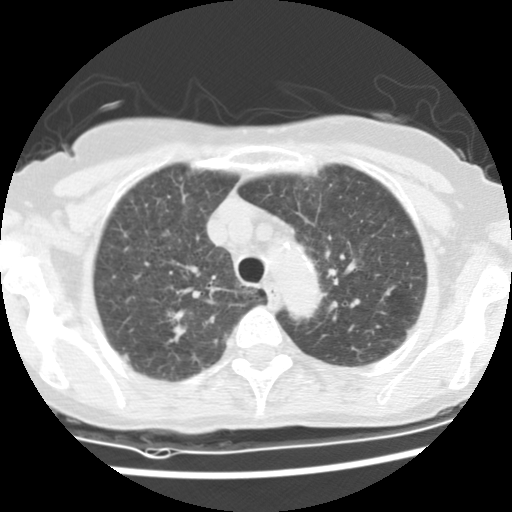
Low-dose screening chest CT, one axial slice; slice 108 of 134 in the series (ordered by position); reconstruction kernel STANDARD; lung window (W 1500 / L -600 HU); 2.5 mm slice thickness; 512 × 512 image matrix, field of view 298 × 298 mm.
Outlined on this slice (expert manual segmentation):
- lesion 1 (tumor, upper lobe of right lung): bounding box (x1, y1, x2, y2) in pixels: (166, 308, 188, 334)